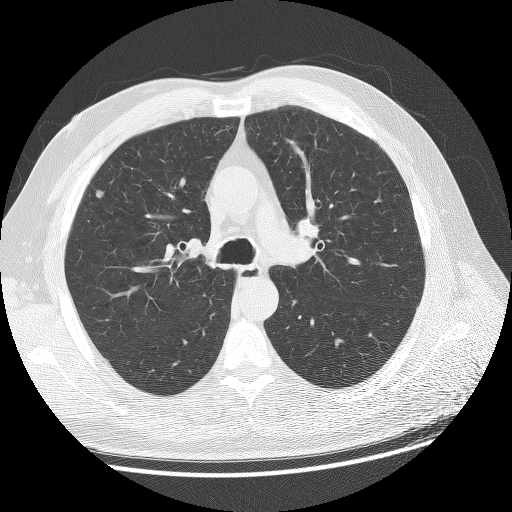
Low-dose screening chest CT, one axial slice; position 96 of 137 along the scan axis; reconstruction kernel BONE; lung window (W 1500 / L -600 HU); 2.5 mm slice thickness; 512 × 512 image matrix, field of view 380 × 380 mm.
Structures marked on this image (outlined manually by an expert reader):
- lesion 1 (tumor): bounding box (x1, y1, x2, y2) in pixels: (96, 191, 103, 198)